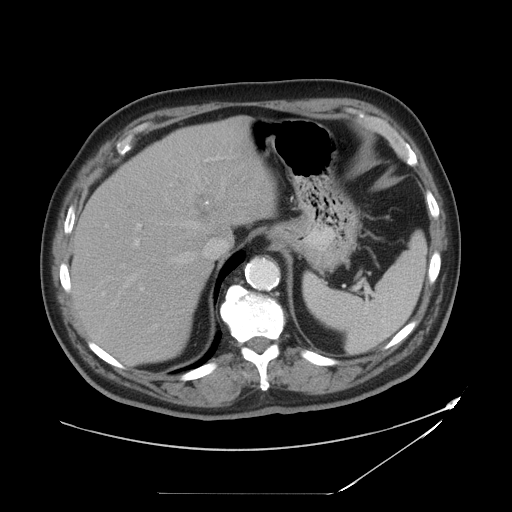
Contrast-enhanced abdominal CT, one axial slice; slice 34 of 49 in the series (ordered by position); intravenous contrast given; soft-tissue window (W 400 / L 40 HU); 5 mm slice thickness; 512 × 512 image matrix, field of view 461 × 461 mm. Male patient, age 72 years. Case-level facts recorded for this patient, not image findings: diagnosis: colorectal cancer liver metastases, imaged before liver resection; multiple liver metastases: no; largest metastasis: 2.5 cm; disease in both lobes: no.
Outlined on this slice (outlined manually by an expert reader):
- hepatic veins: box from (x=123, y=163) to (x=219, y=288) px
- liver: (x=73, y=118)–(x=274, y=364)
- planned liver remnant (the part of the liver to remain after resection): (x=73, y=175)–(x=210, y=364)
- portal vein (with intrahepatic branches): (x=134, y=155)–(x=222, y=291)
- liver metastasis: (x=195, y=192)–(x=219, y=218)